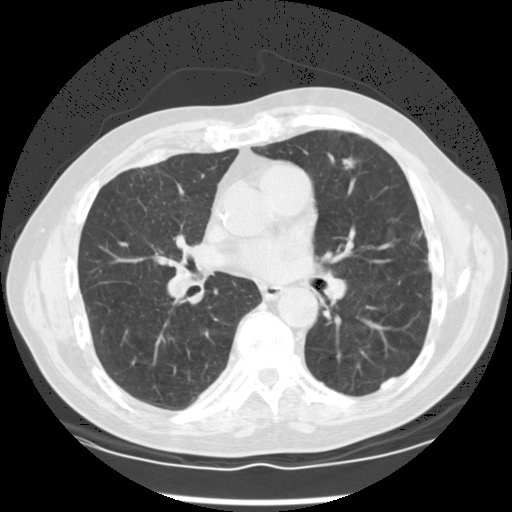
Chest CT (low-dose screening protocol), one axial image. Third screening round (two years after baseline). Lung window (W 1500 / L -600 HU). 2.5 mm slice thickness. Standard (soft-tissue) reconstruction kernel (STANDARD). Slice 66 of 120 in the series. Male, age 68 years at enrolment. Former smoker at enrolment.
Expert-annotated lung lesion, box from (x=322, y=149) to (x=370, y=192) px. Screening reader's record for this exam (one nodule recorded; not confirmed to be the boxed lesion): non-calcified nodule or mass ≥4 mm, left upper lobe, 10 × 8 mm, spiculated (stellate) margins, soft tissue attenuation, pre-existing on the prior screen: no. Official screen result: positive, other.